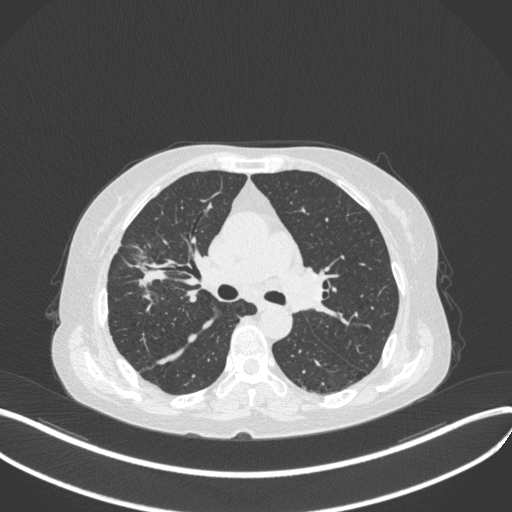
Chest CT, one axial slice. Position 246 of 429 along the scan axis. Reconstruction kernel B31f. 120 kVp. Lung window (W 1500 / L -600 HU). 1 mm slice thickness. 512 × 512 image matrix, field of view 400 × 400 mm. Female patient, age 69 years. Case-level facts recorded for this patient, not image findings: clinical TNM (as recorded): T1b N3 M0.
Outlined on this slice (rectangle marked by the reading radiologist):
- lung tumour (recorded histology: small cell carcinoma): bounding box <125,253,171,296> (left, top, right, bottom; pixels)